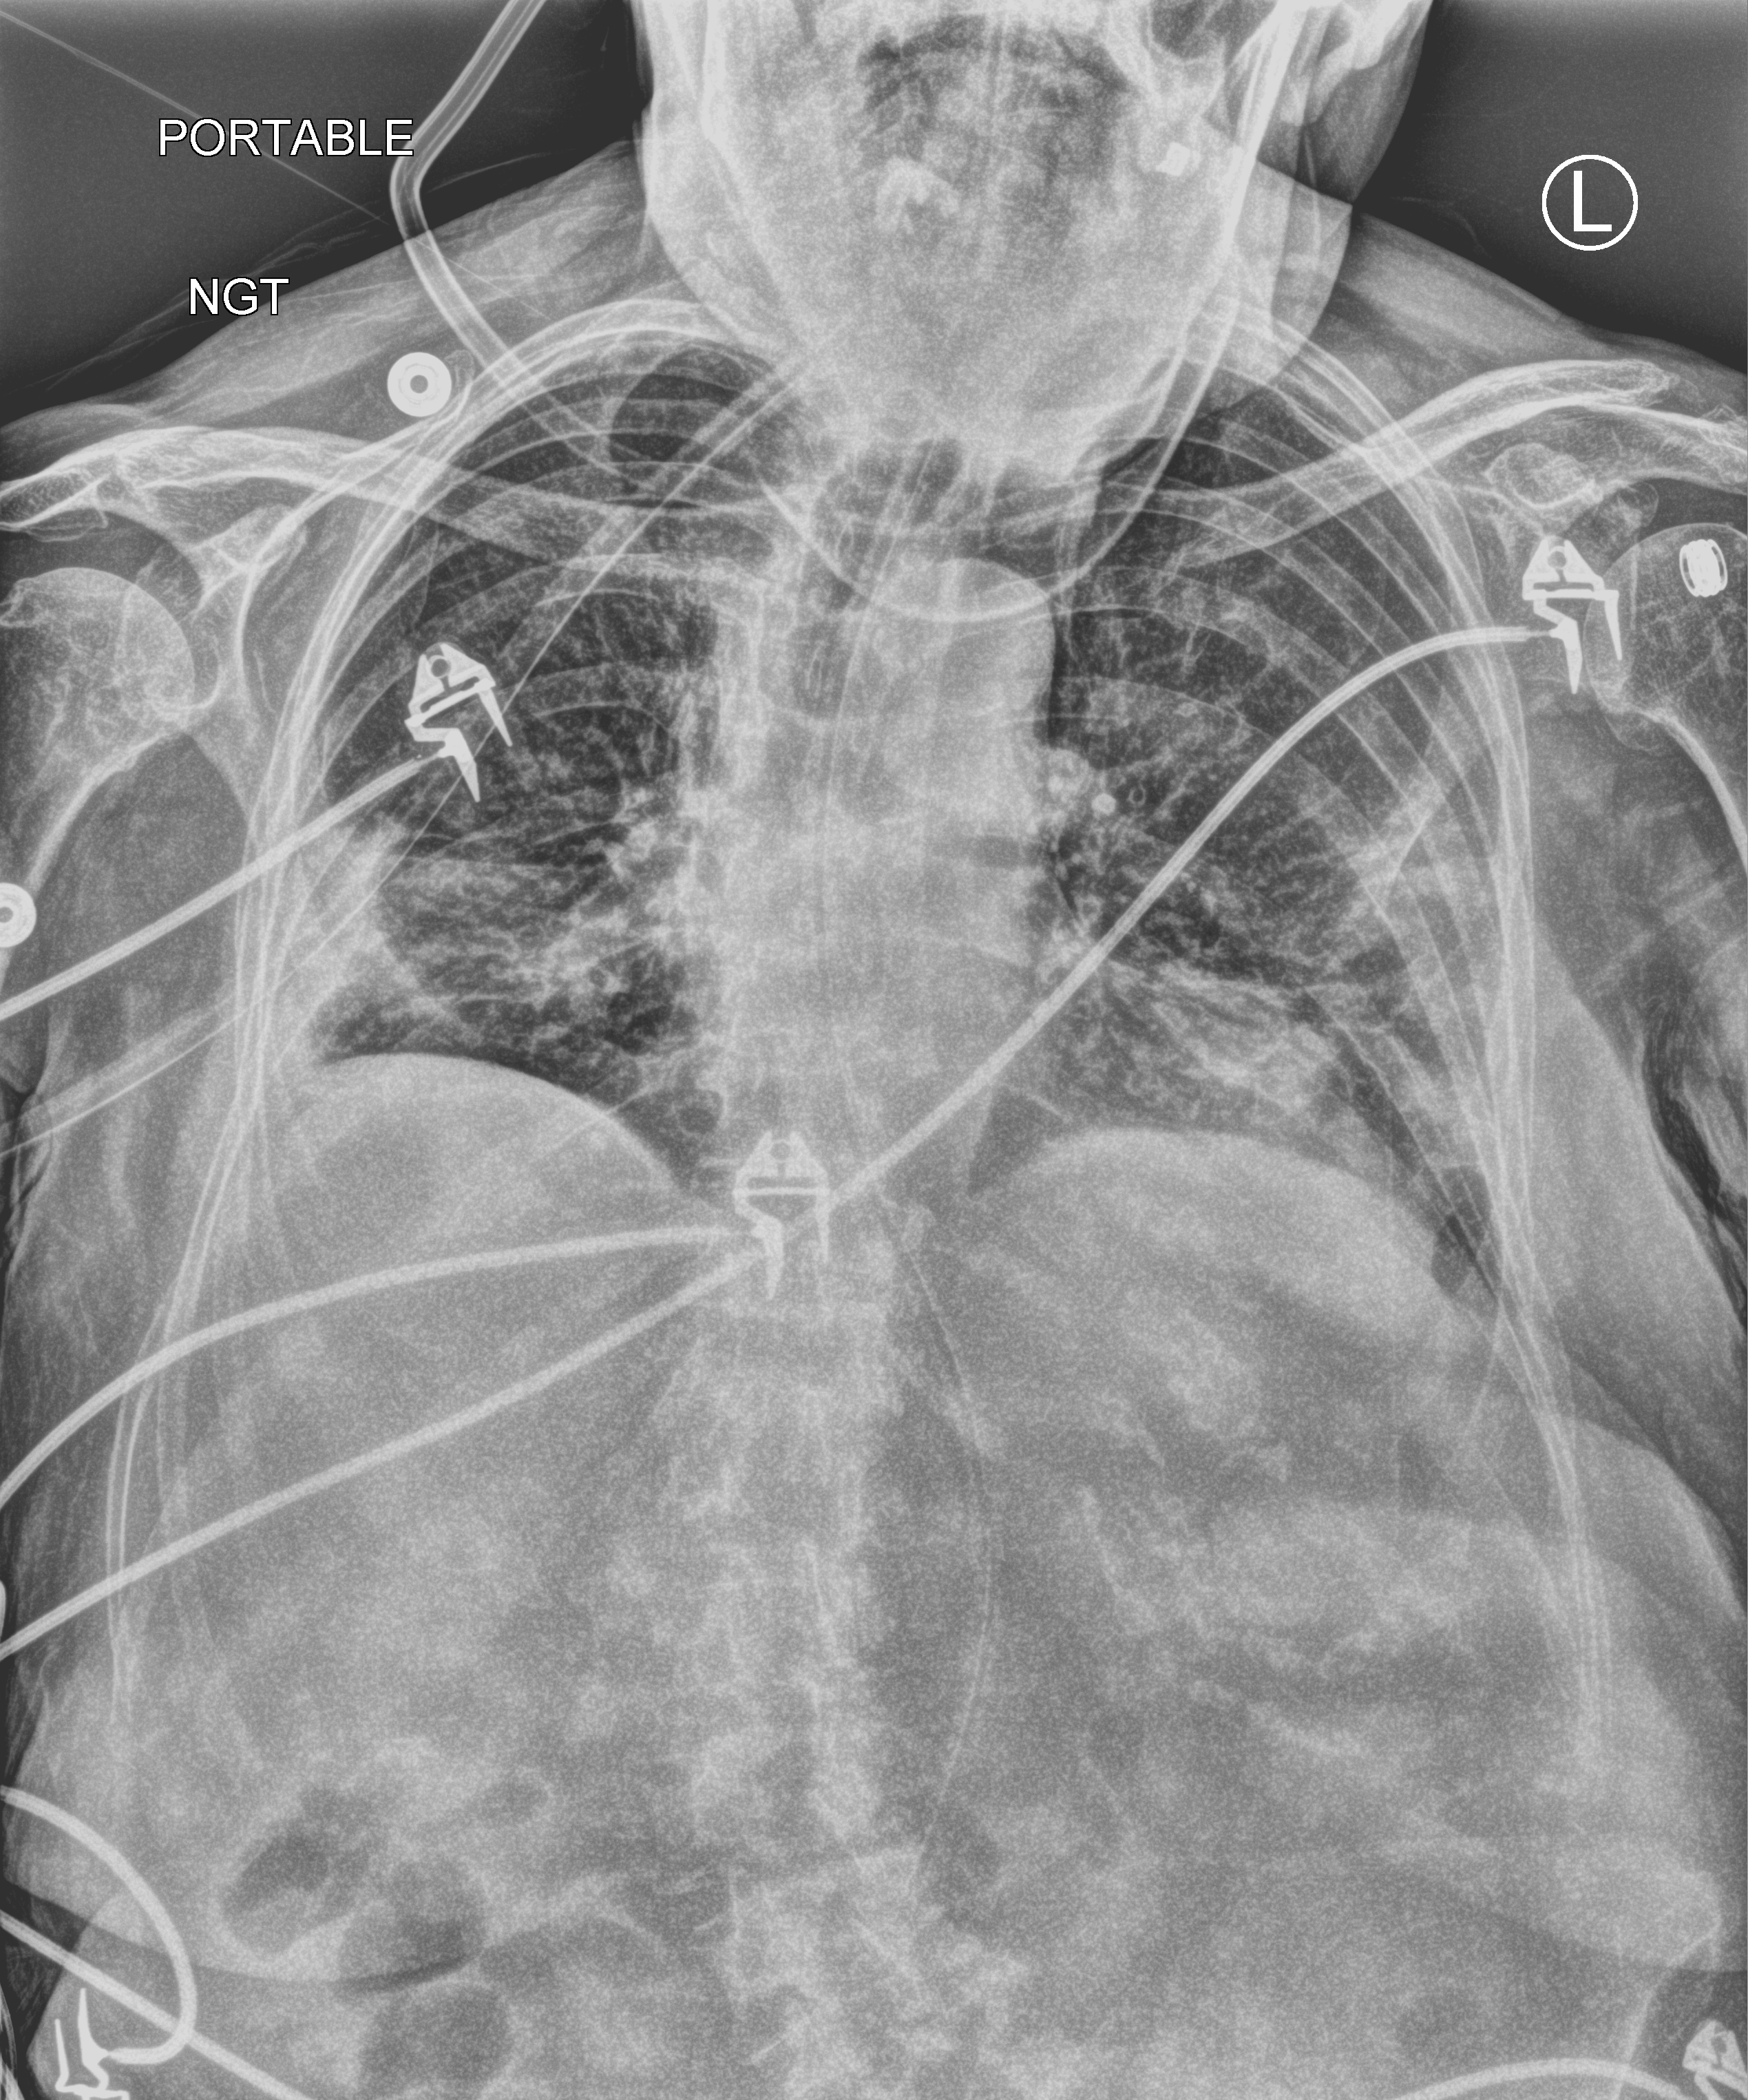
Bedside chest radiograph (computed radiography), anteroposterior (AP) projection. Patient hospitalised with COVID-19; female, aged 75–90 years.
Admission-level facts for this patient (not findings on this image; timing relative to this image not recorded): admitted to intensive care during this hospital stay: yes; hypertension (admission record): yes.